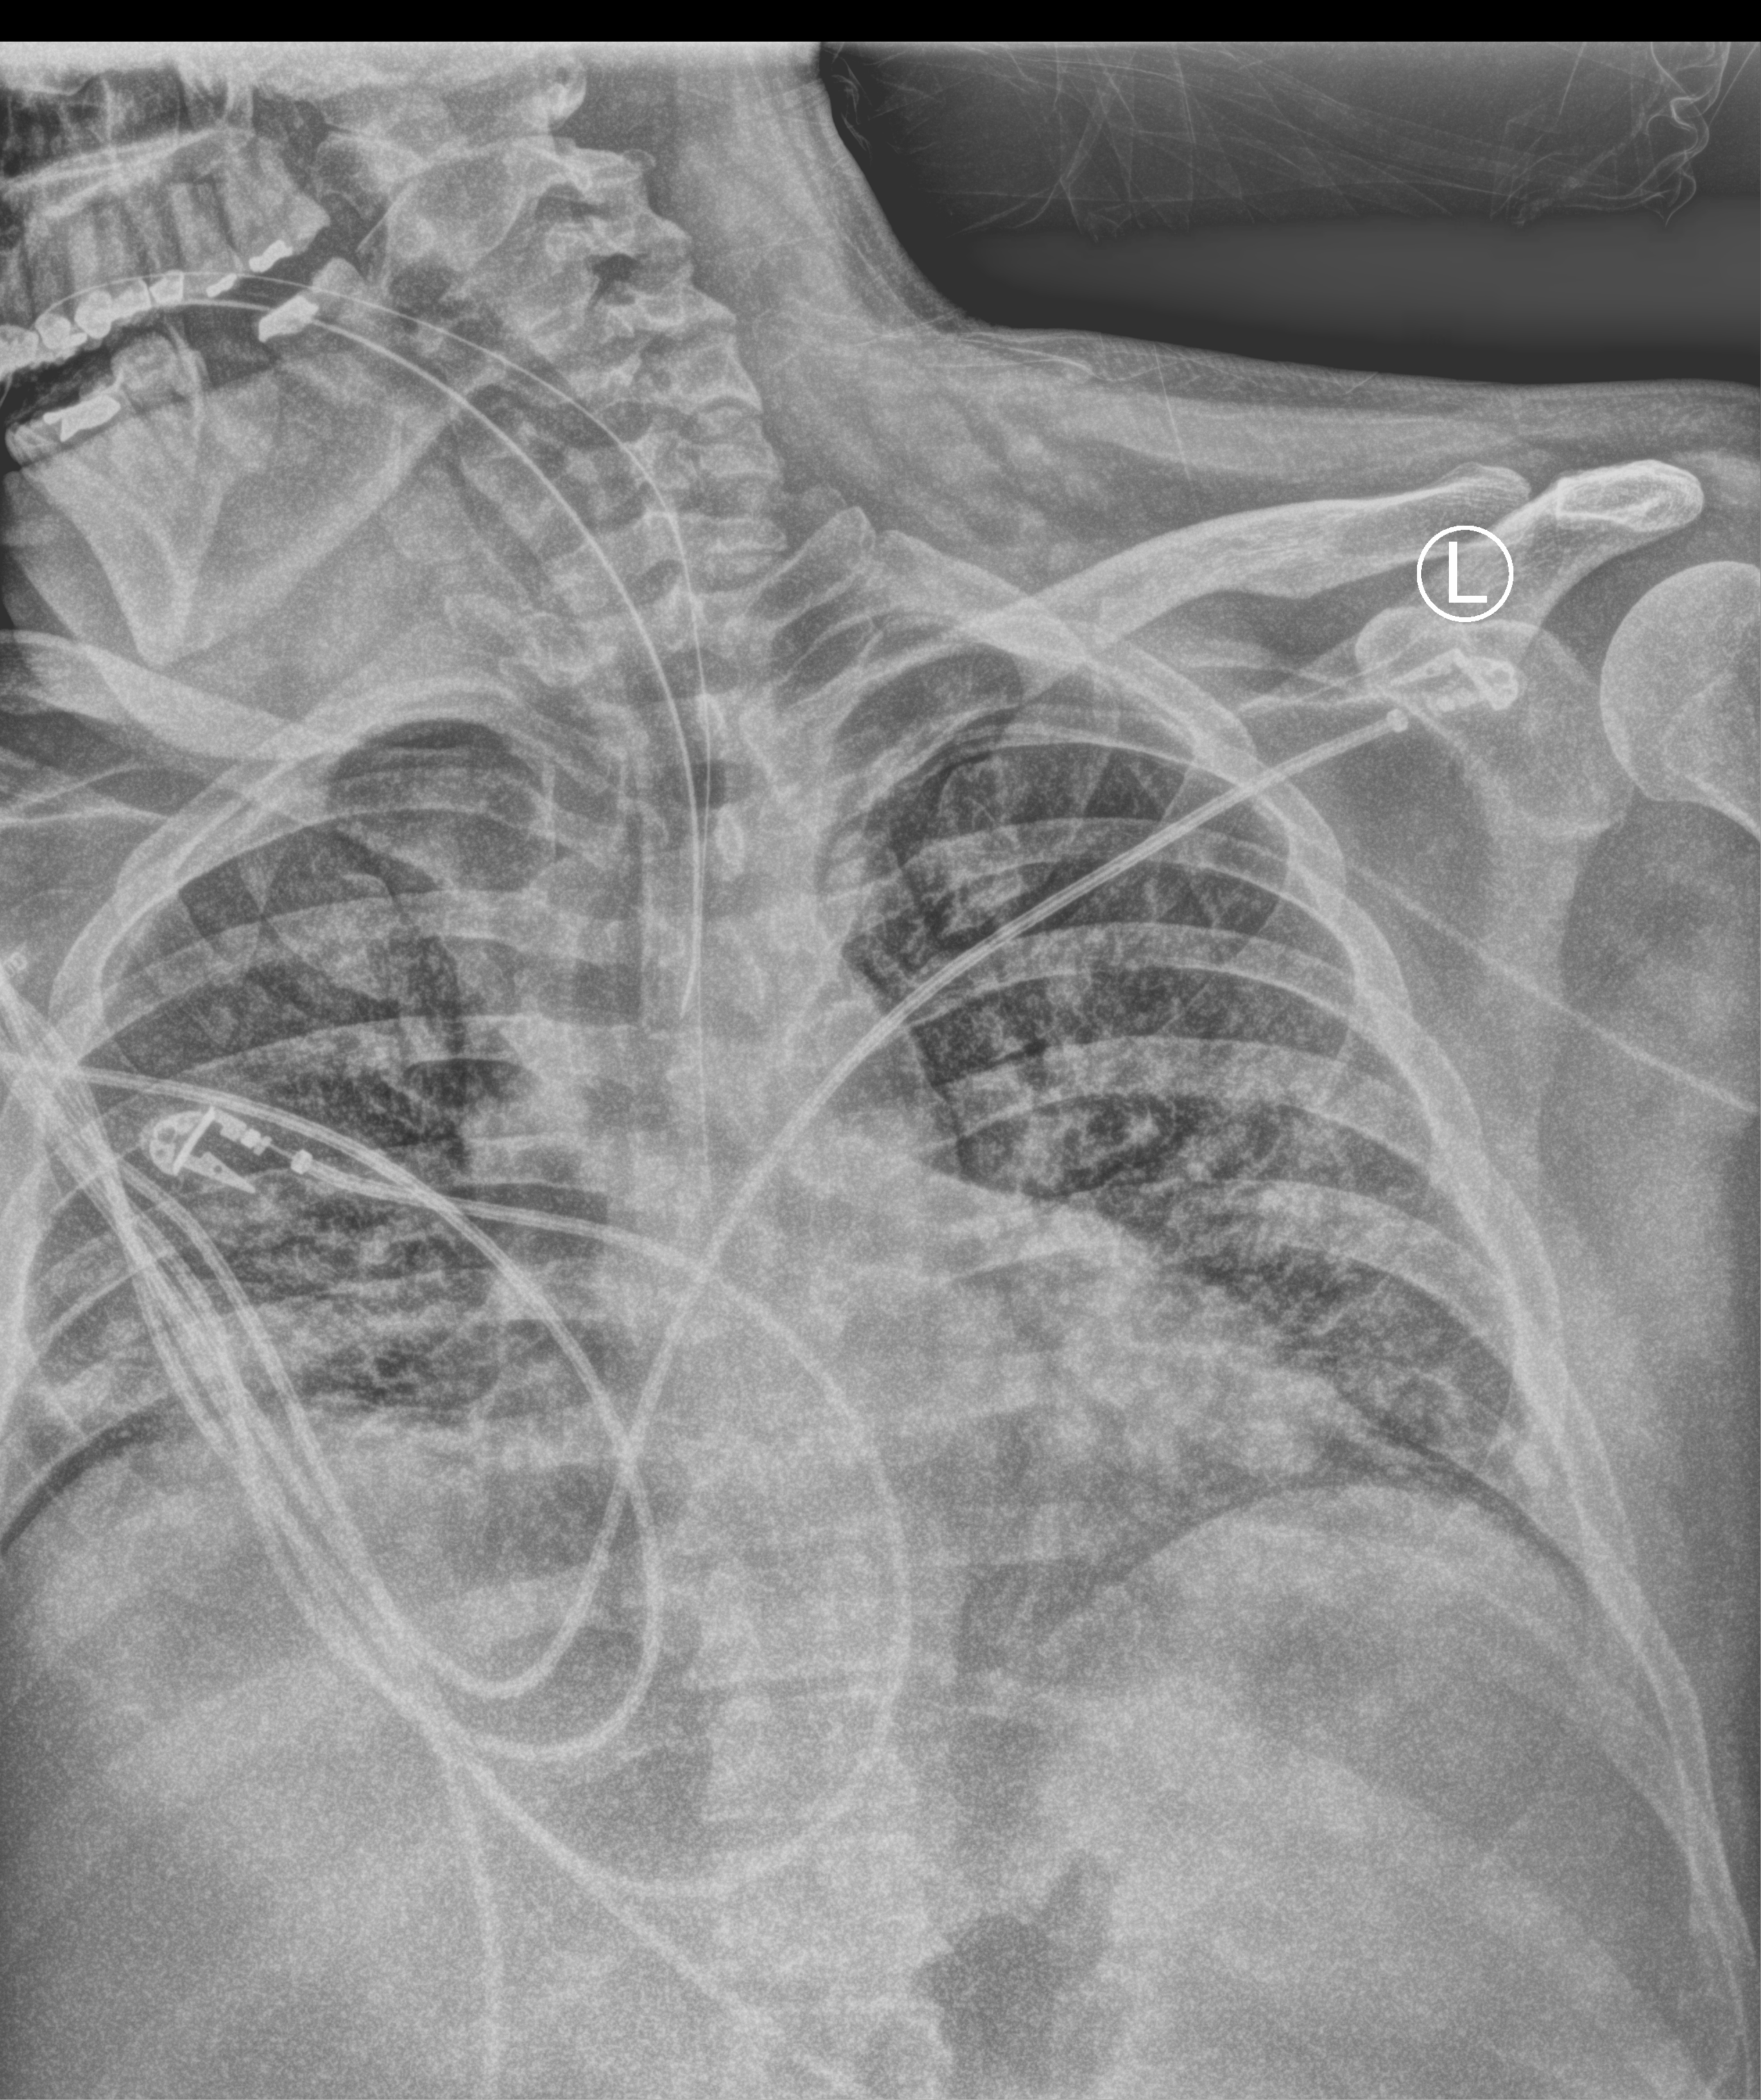
Bedside chest radiograph (computed radiography), anteroposterior (AP) projection. Male patient hospitalised with COVID-19, age 18–59 years.
Hospital-stay facts (about this admission, not read from this image; timing relative to this image not recorded):
- admitted to intensive care during this hospital stay: yes
- COPD (admission record): no
- mechanically ventilated during this hospital stay: yes